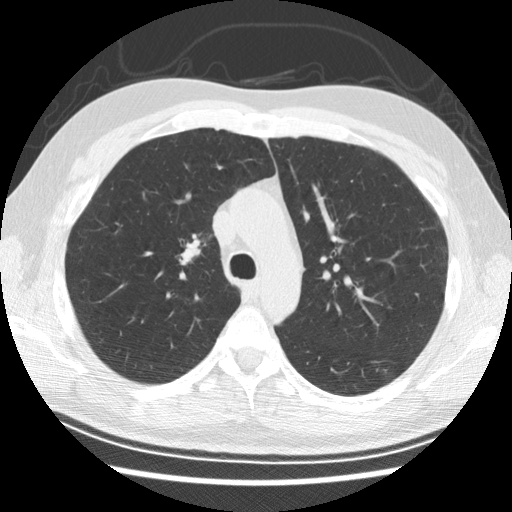
Axial slice from a low-dose chest CT screening exam. Baseline annual screen. Lung window (W 1500 / L -600 HU). 2.5 mm slice thickness. Standard (soft-tissue) reconstruction kernel (STANDARD). Slice 87 of 278 in the series. 512 × 512 image matrix, field of view 340 × 340 mm. Male participant, aged 57 years at enrolment. Former smoker at enrolment.
Expert-annotated lung lesion, bounding box <163,221,221,280> (left, top, right, bottom; pixels). The screening reader recorded 6 non-calcified nodules or masses ≥4 mm on this exam; which of them this box marks is not recorded. Official screen result: negative screen, minor abnormalities not suspicious for lung cancer. Later outcome: lung cancer diagnosed 766 days after this screen — adenocarcinoma, NOS, right upper lobe, poorly differentiated (G3), stage IB (AJCC 6th edition), 25 mm at pathology.